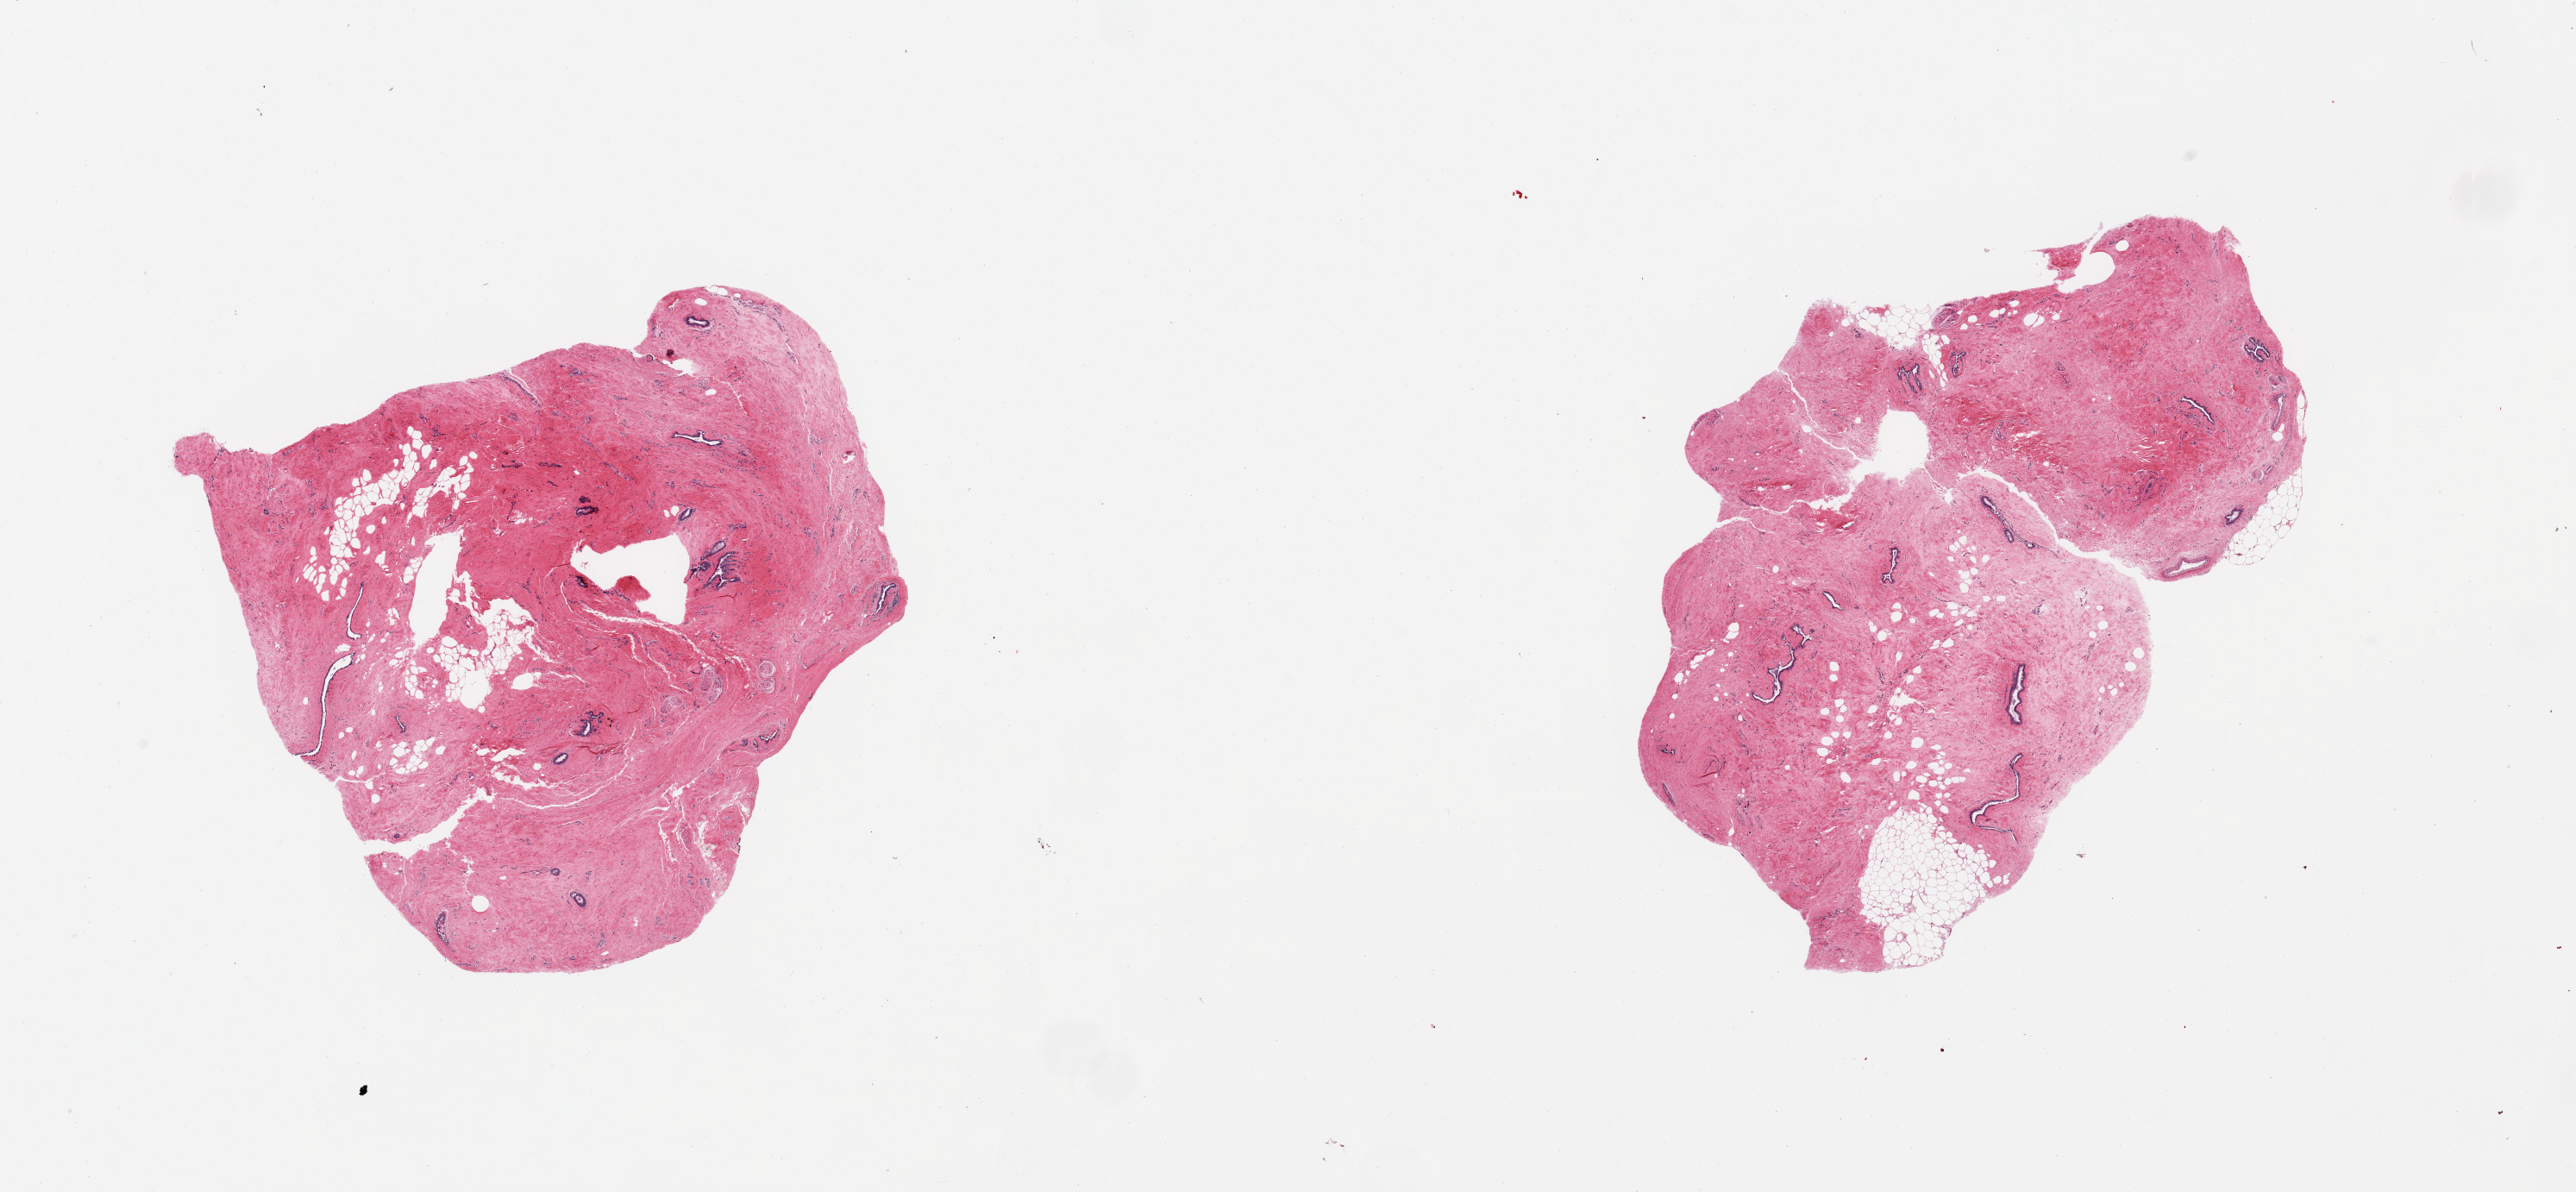
H&E whole-slide image, a low-resolution overview of the entire scanned area, about 23.6 x 10.9 mm. PAXgene-fixed paraffin-embedded (PFPE) section. Target tissue: breast. Donor tissue sample. Male donor.
- reviewer comment on this tissue sample: 2 pieces; gynecomastoid features: fibrous stroma and ducts, 10% fat